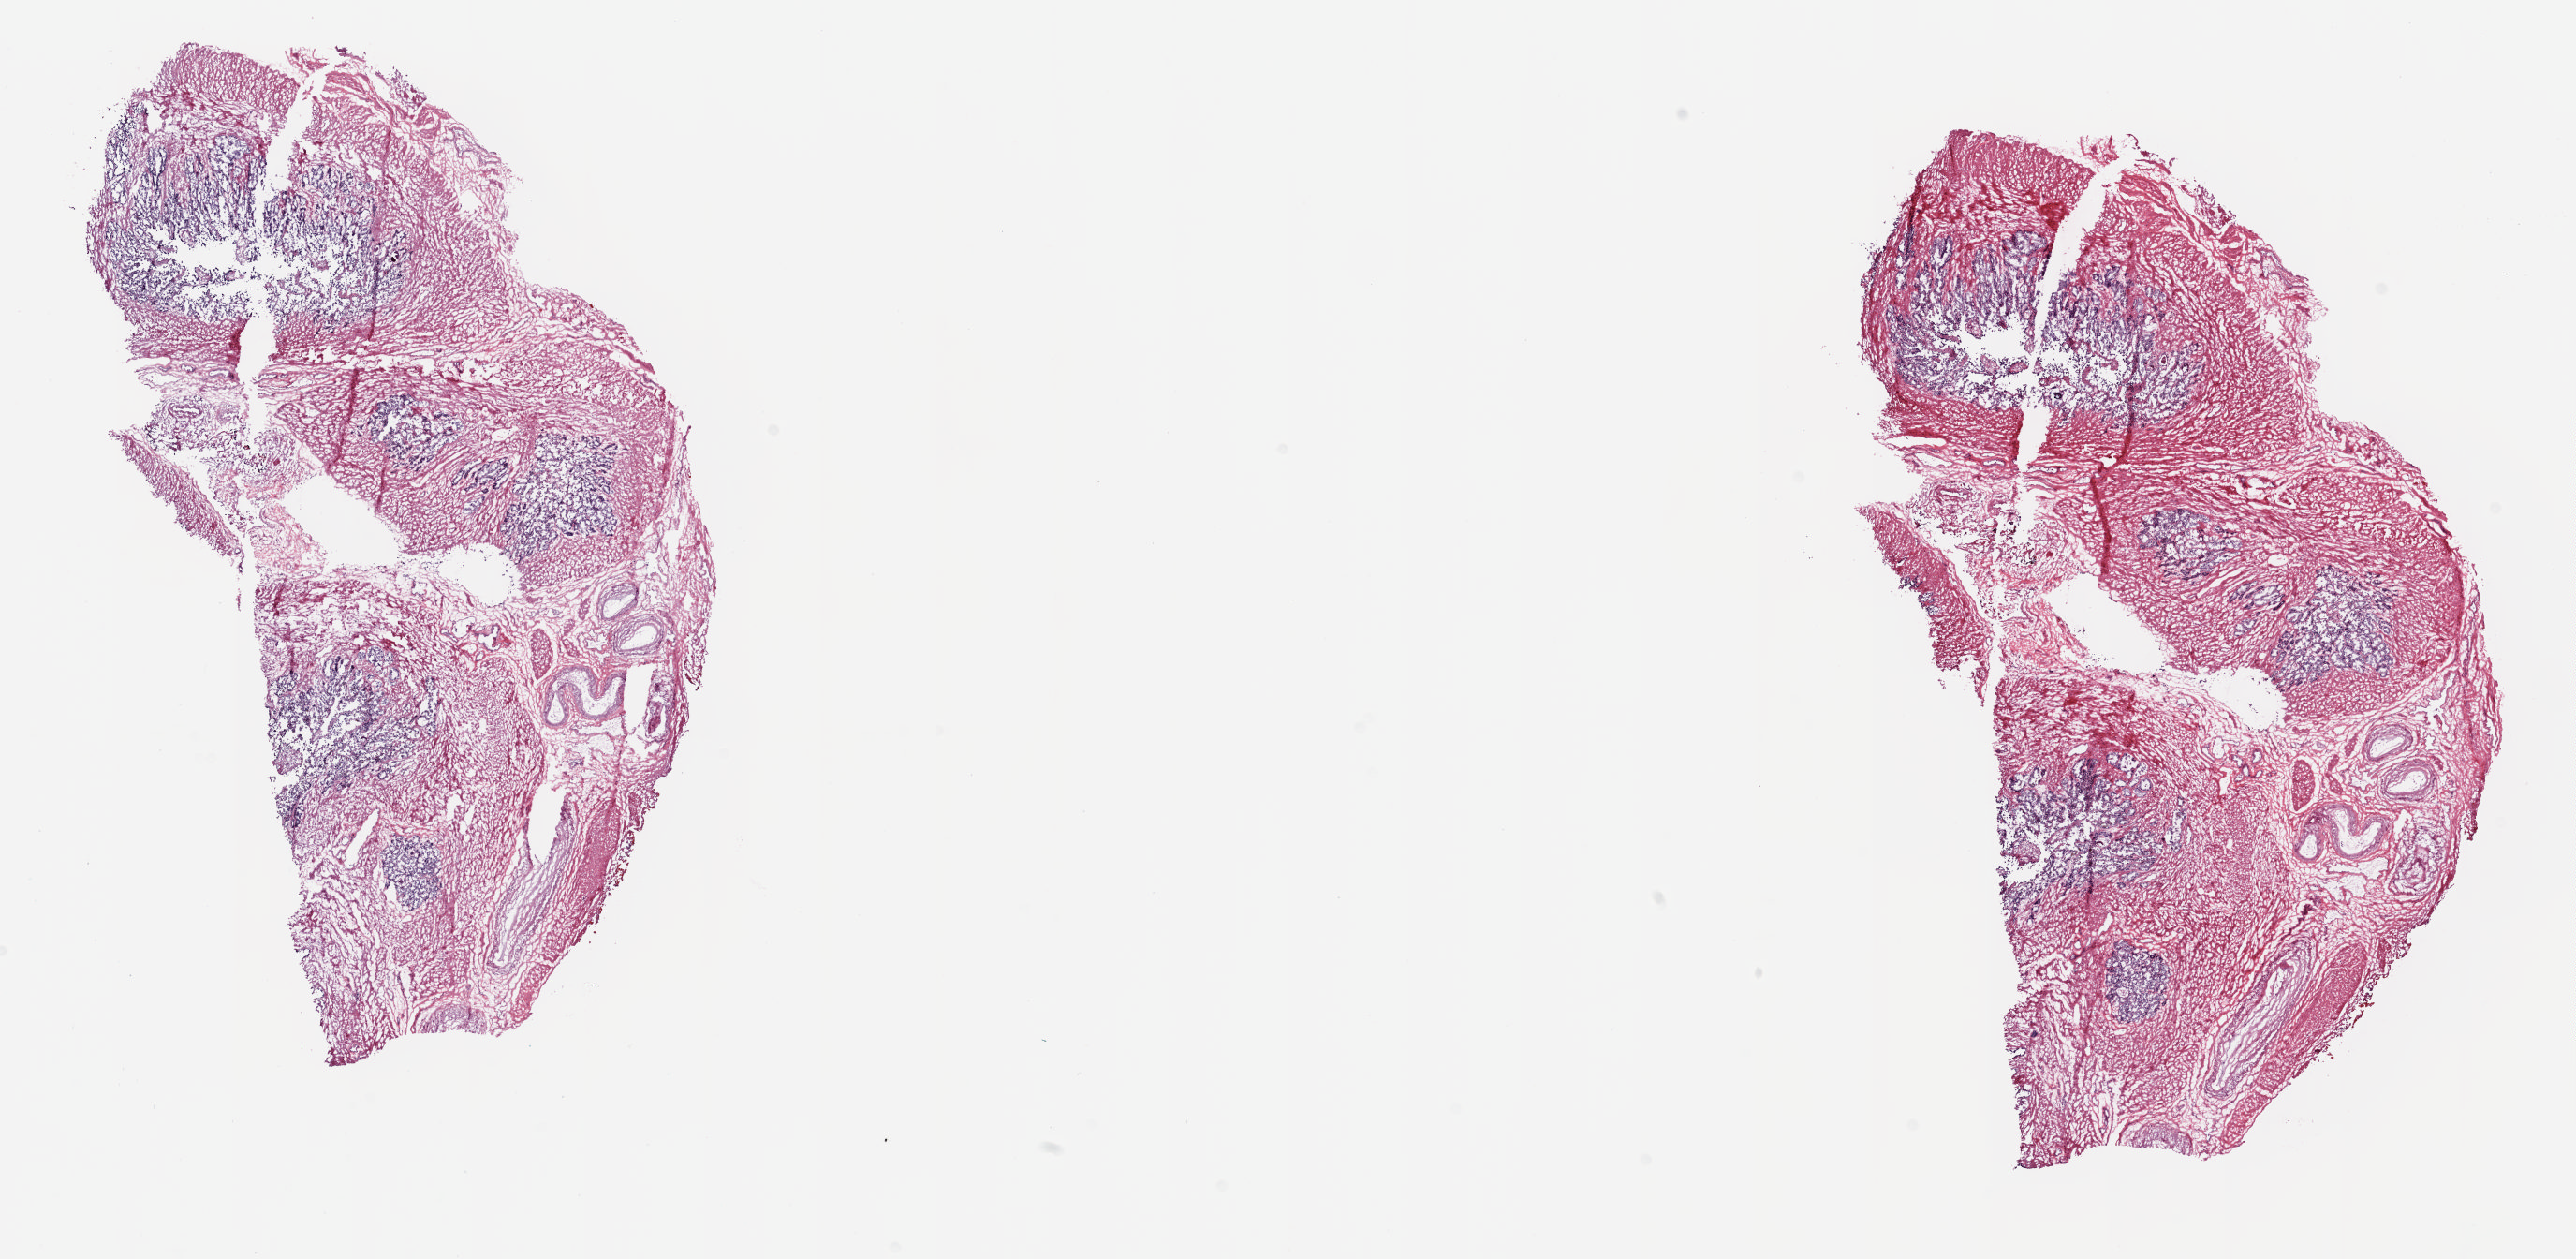
Whole-slide histology image, Hematoxylin and eosin (H&E) stained, shown as a low-resolution overview of the whole scanned area (about 21.8 x 10.7 mm, from a 20x scan); frozen section; sample: solid tissue normal (non-tumour tissue), prostate. Male, age 57 years at initial diagnosis. Slide review estimates, as recorded: tumour cells 0%, tumour nuclei 0%, normal cells 100%, stromal cells 0%, necrosis 0%. Inflammatory infiltration, as recorded: lymphocyte infiltration 0%, monocyte infiltration 0%, neutrophil infiltration 0%.
This section: solid tissue normal sample (biorepository sample class). Patient diagnosis: Adenocarcinoma, NOS.